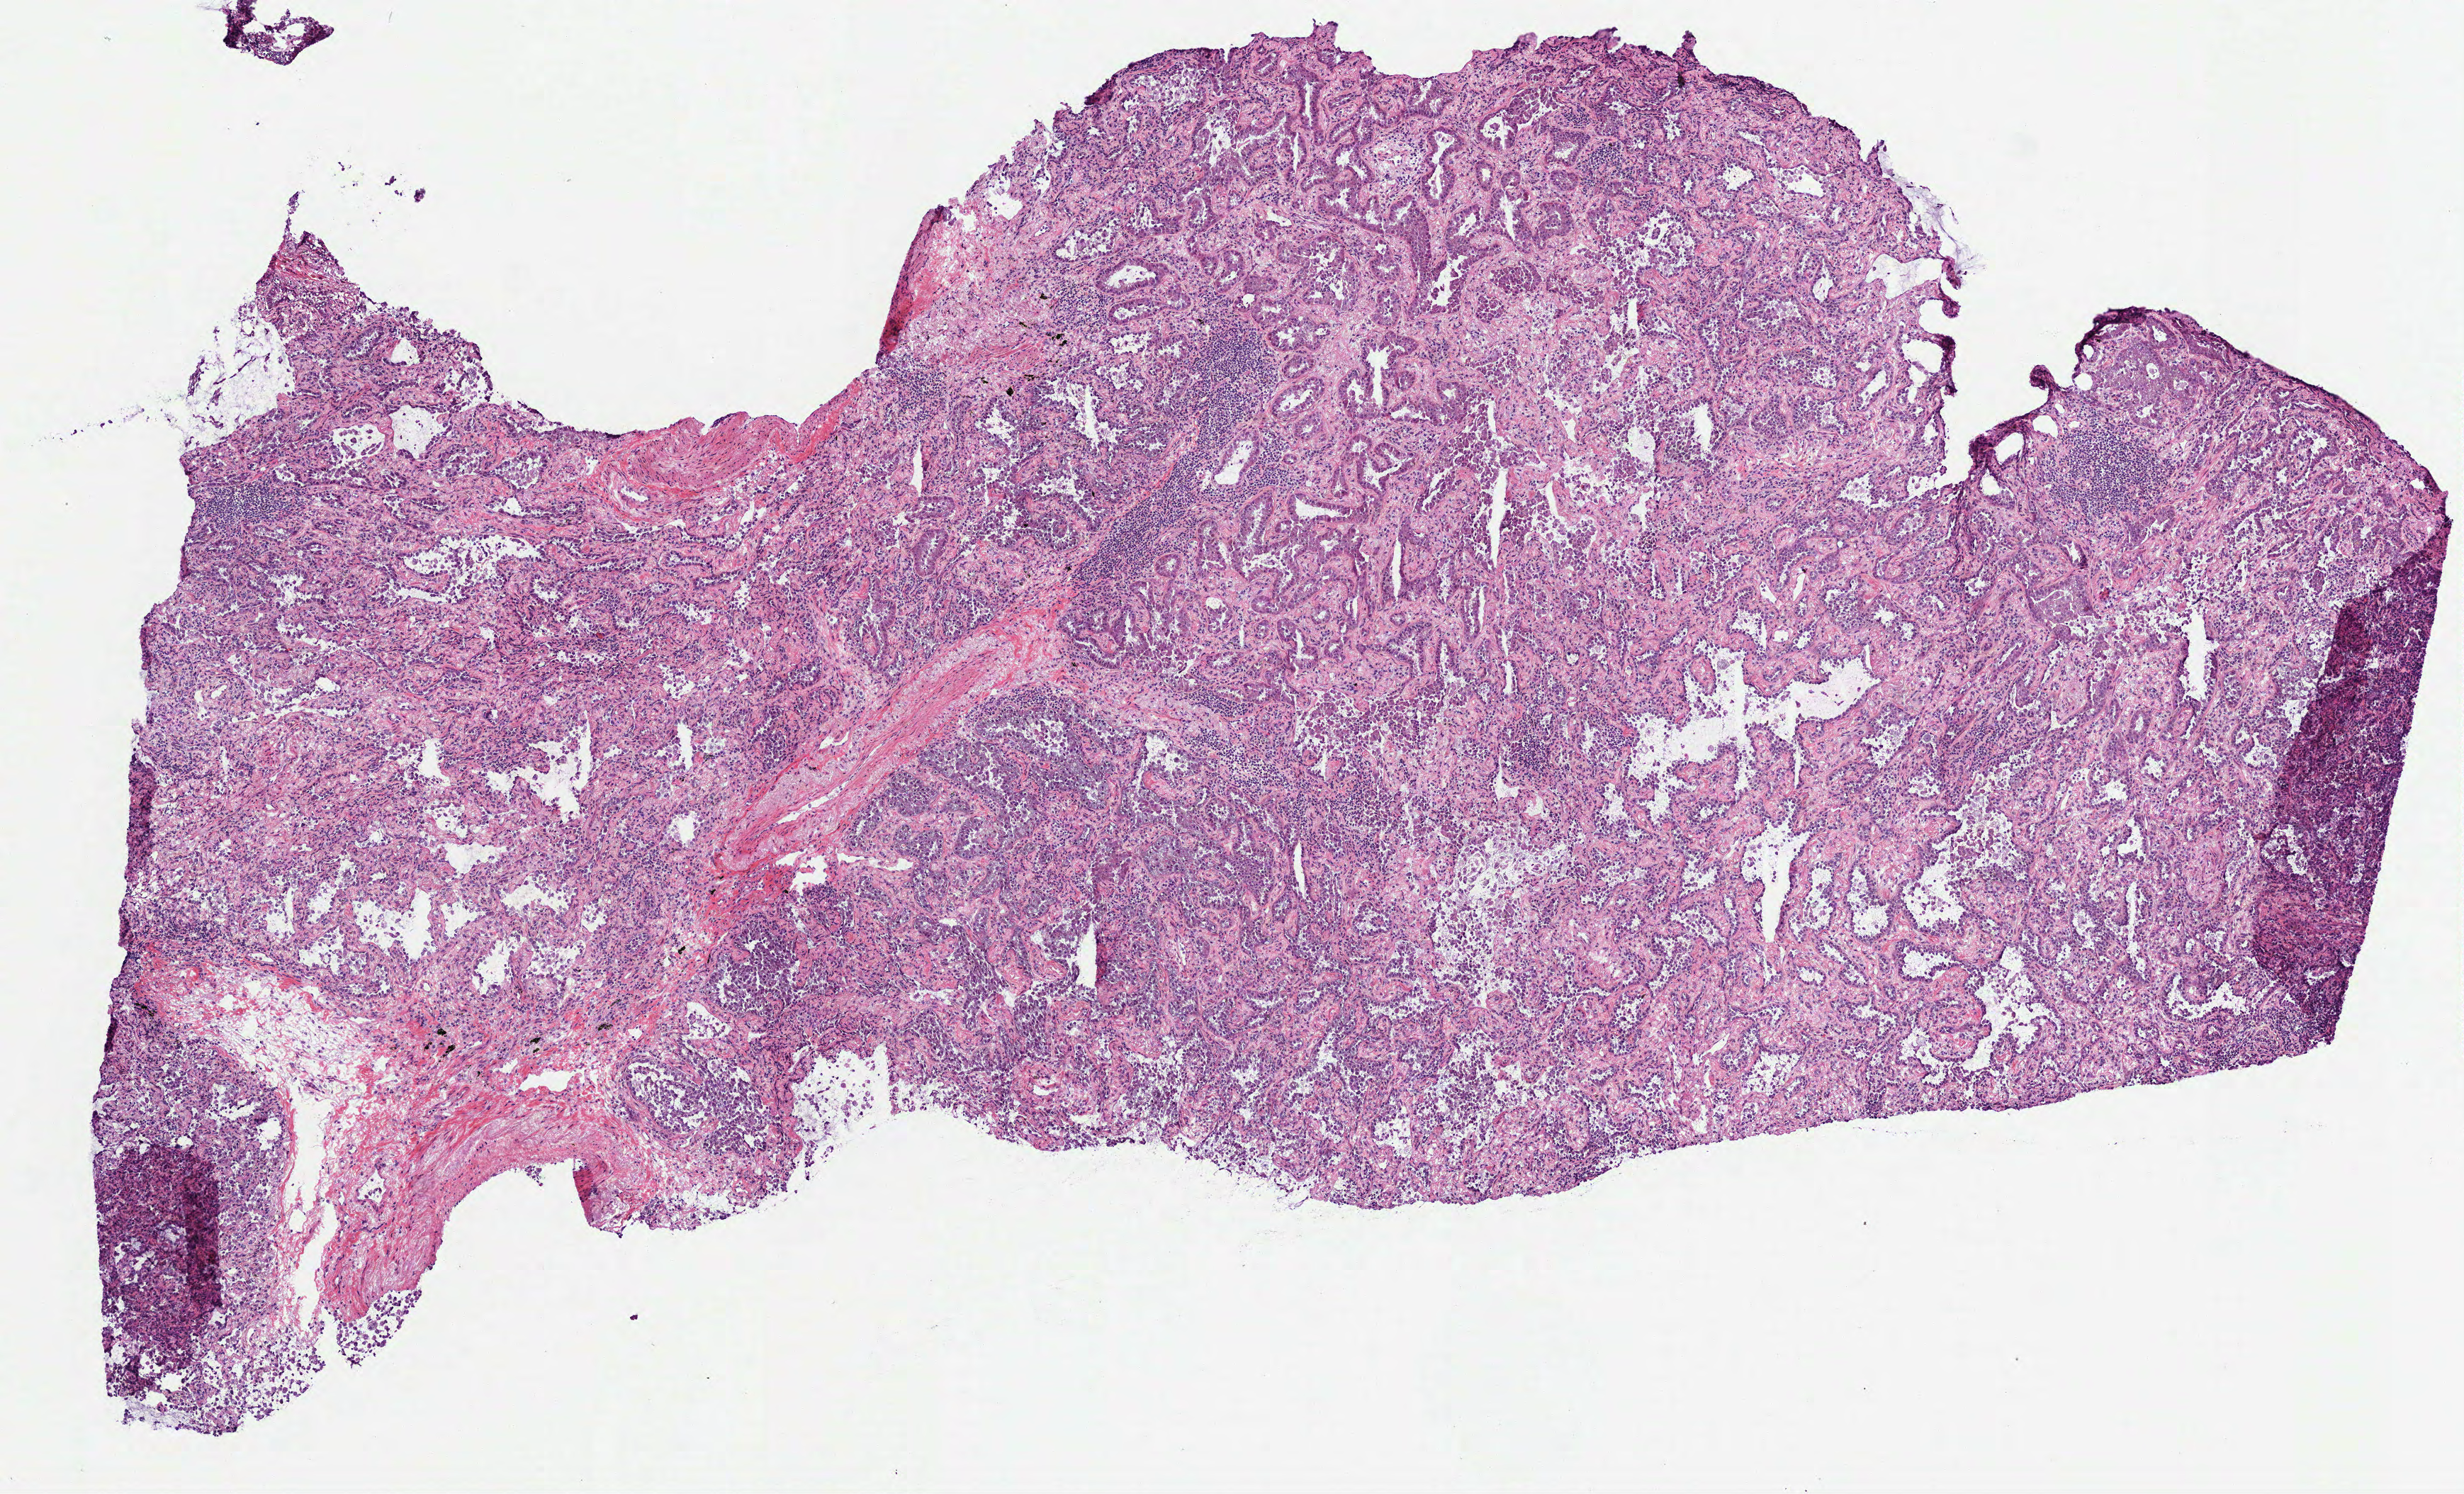
Whole-slide histology image, H&E-stained, low-resolution overview of the scanned area, about 7.0 x 4.3 mm (slide scanned at 40x). Frozen section from the top of the tissue portion. Sample: primary tumour, lung. Female, age 75 years at initial diagnosis. Pathologist review of this section (percent, as recorded): tumour cells 85%, tumour nuclei 75%, normal cells 0%, stromal cells 15%, necrosis 0%.
AJCC pathologic stage: IA (7th edition). Histologic diagnosis: Adenocarcinoma, NOS (upper lobe, lung). TNM: T1a N0 MX.